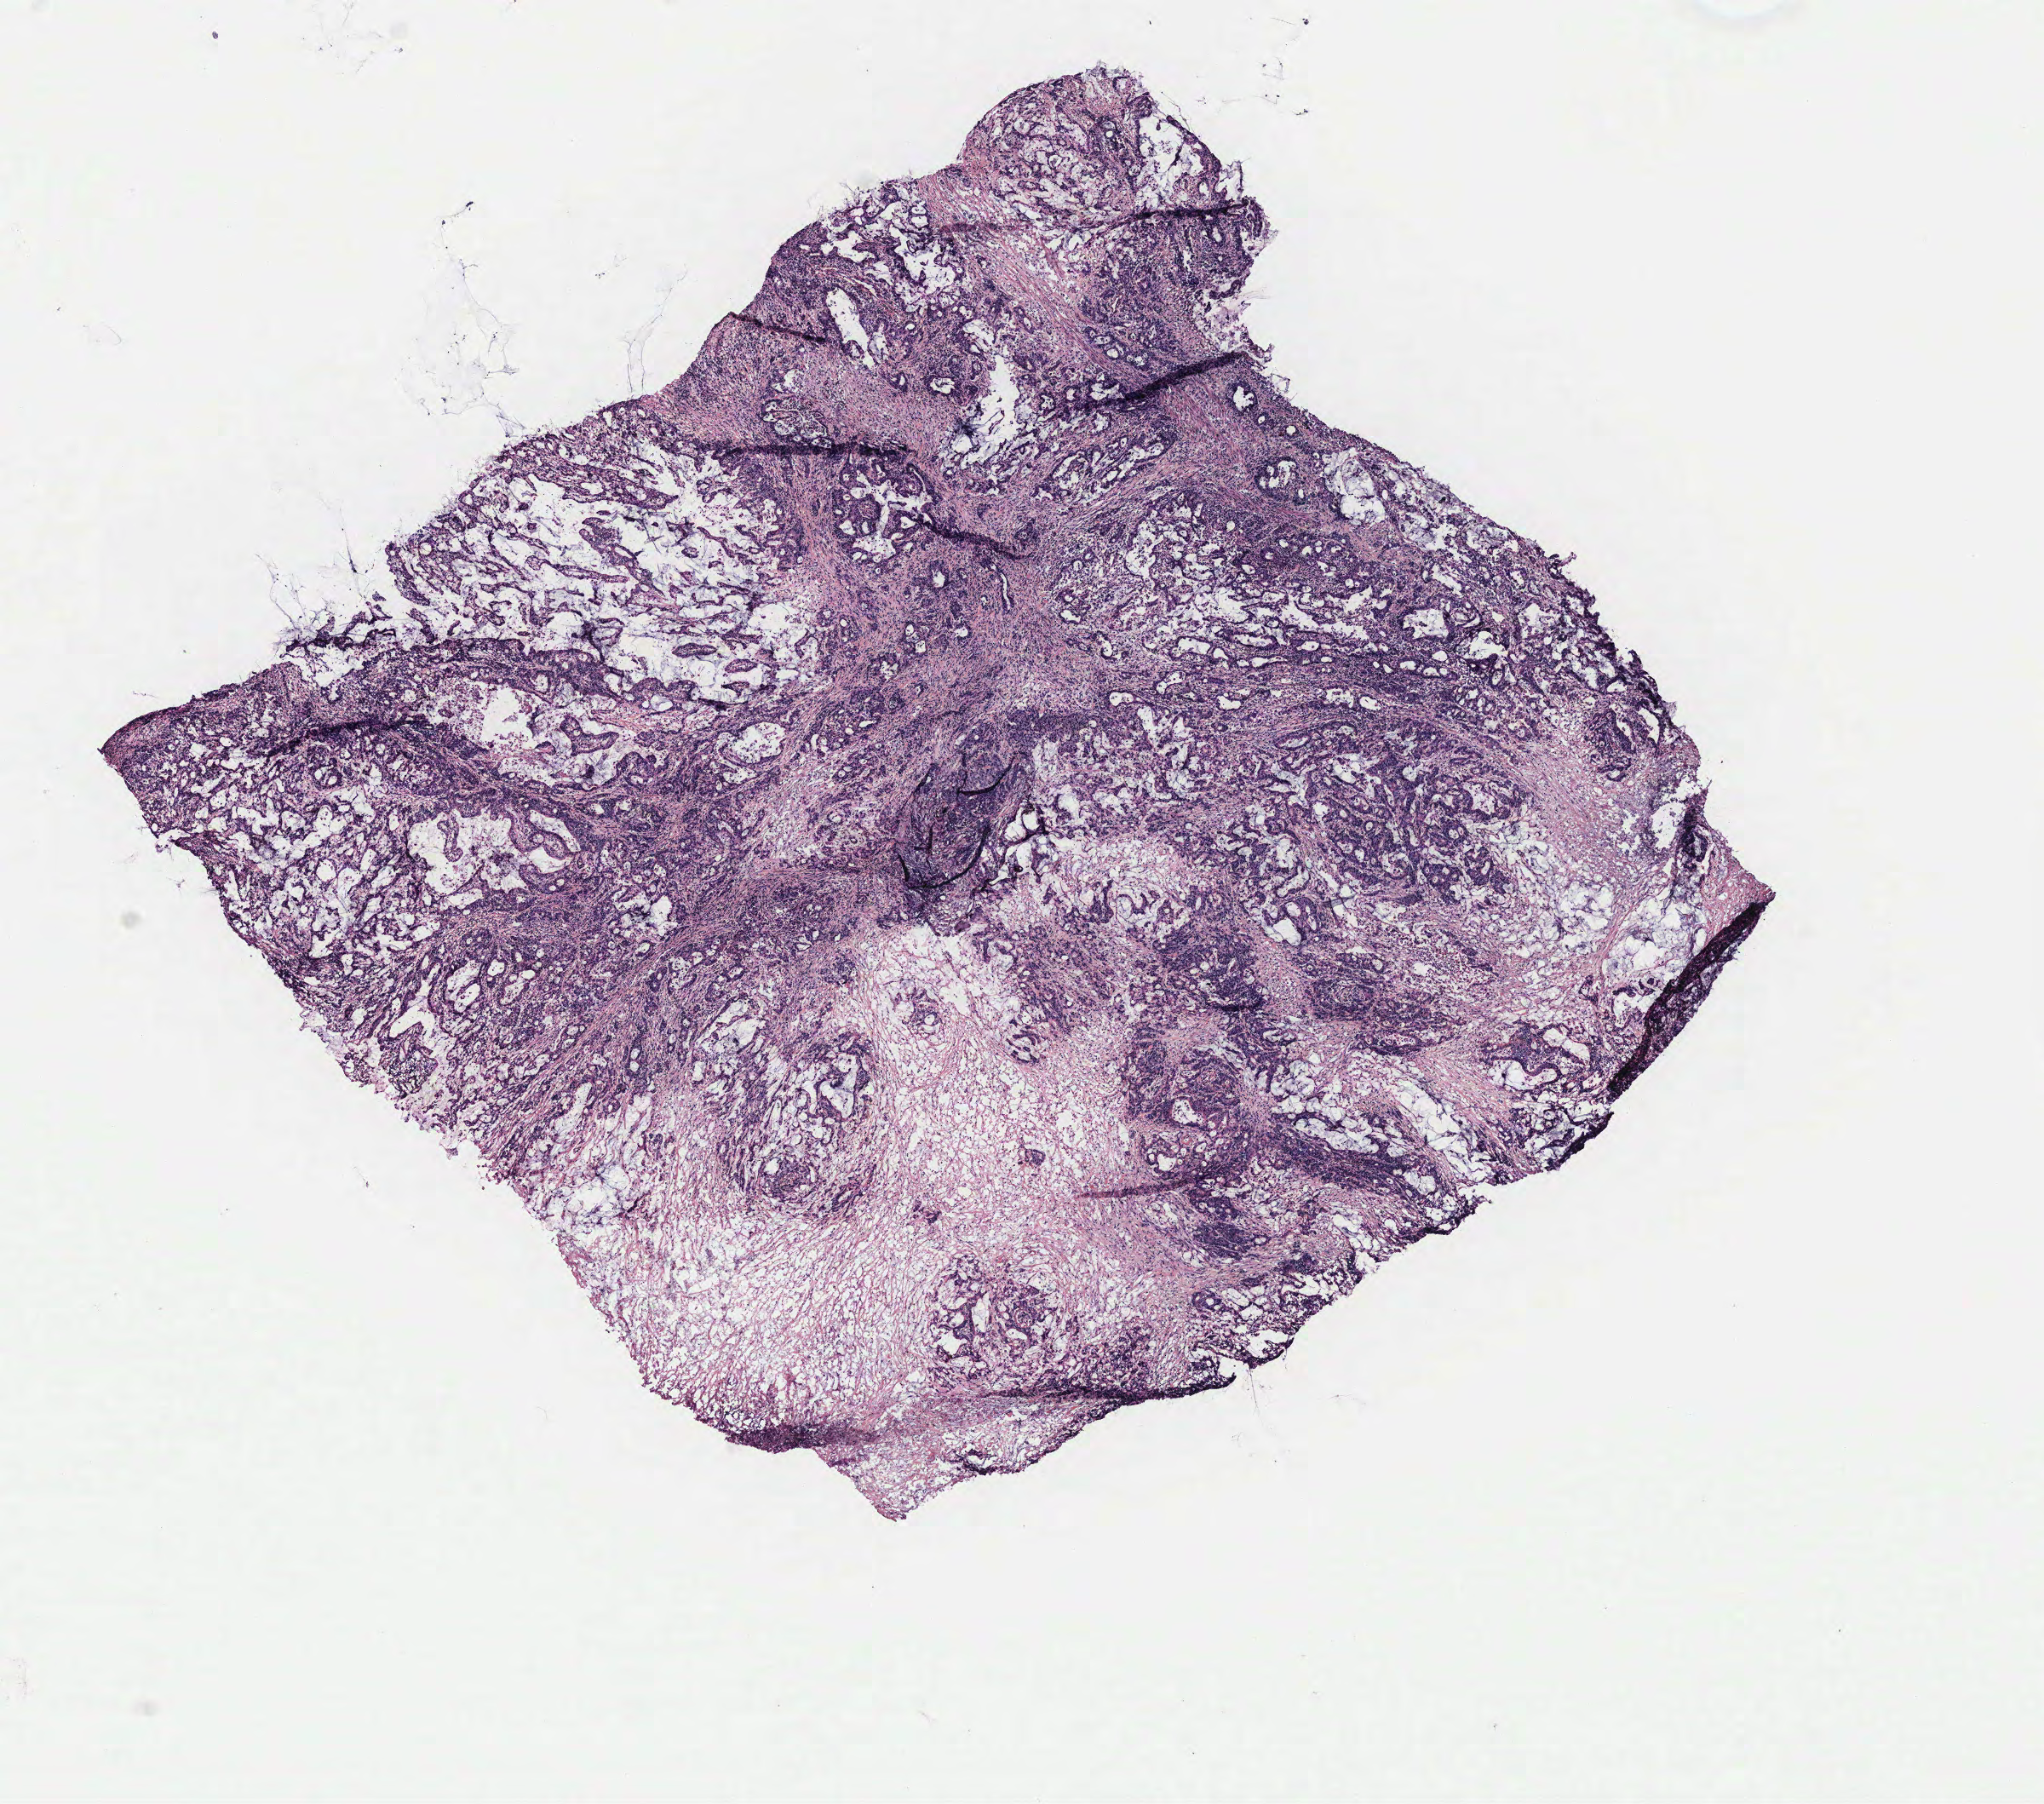
Digitized H&E-stained tissue section (whole slide), whole scanned area (about 9.6 x 8.5 mm, slide scanned at 40x) shown as a low-resolution overview, colon, tumour tissue. 85-year-old female patient.
Histologic diagnosis: Adenocarcinoma, NOS.